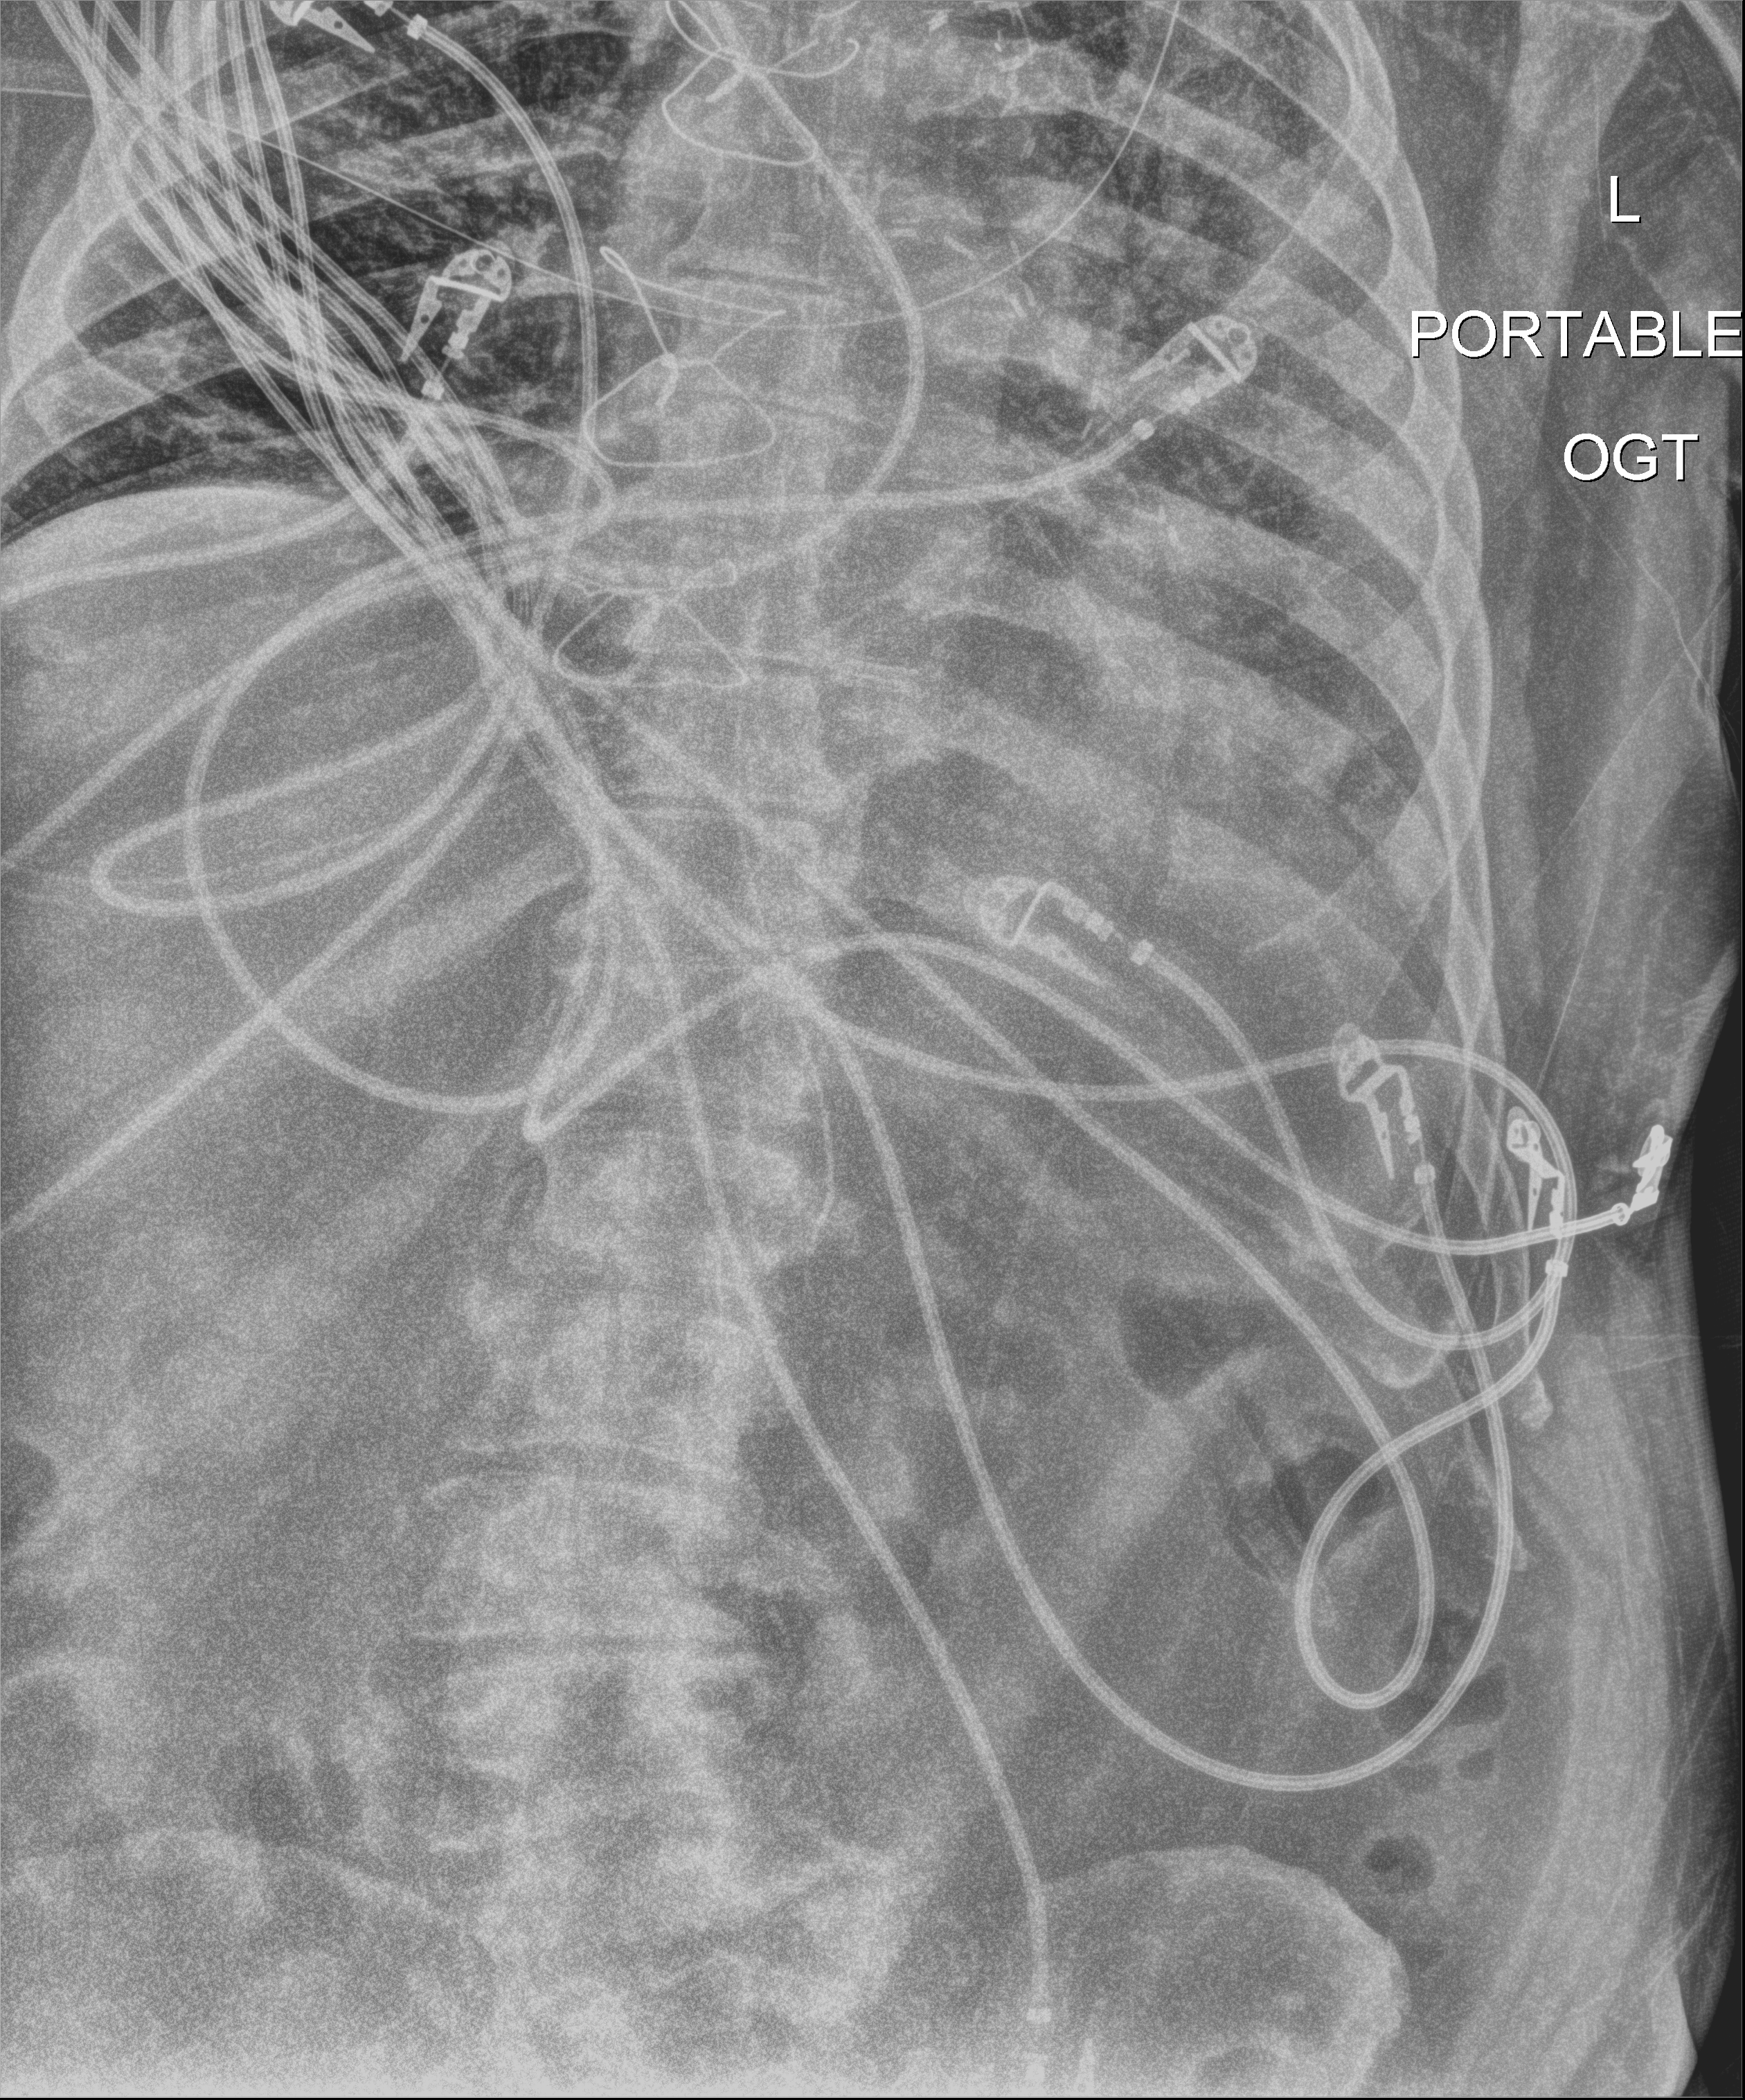
Portable chest radiograph, anteroposterior (AP) projection. Male patient hospitalised with COVID-19, age 60–74 years.
From the hospital-stay record, not from the radiograph (when in the stay this image was taken is not recorded):
- smoking status (admission record): former